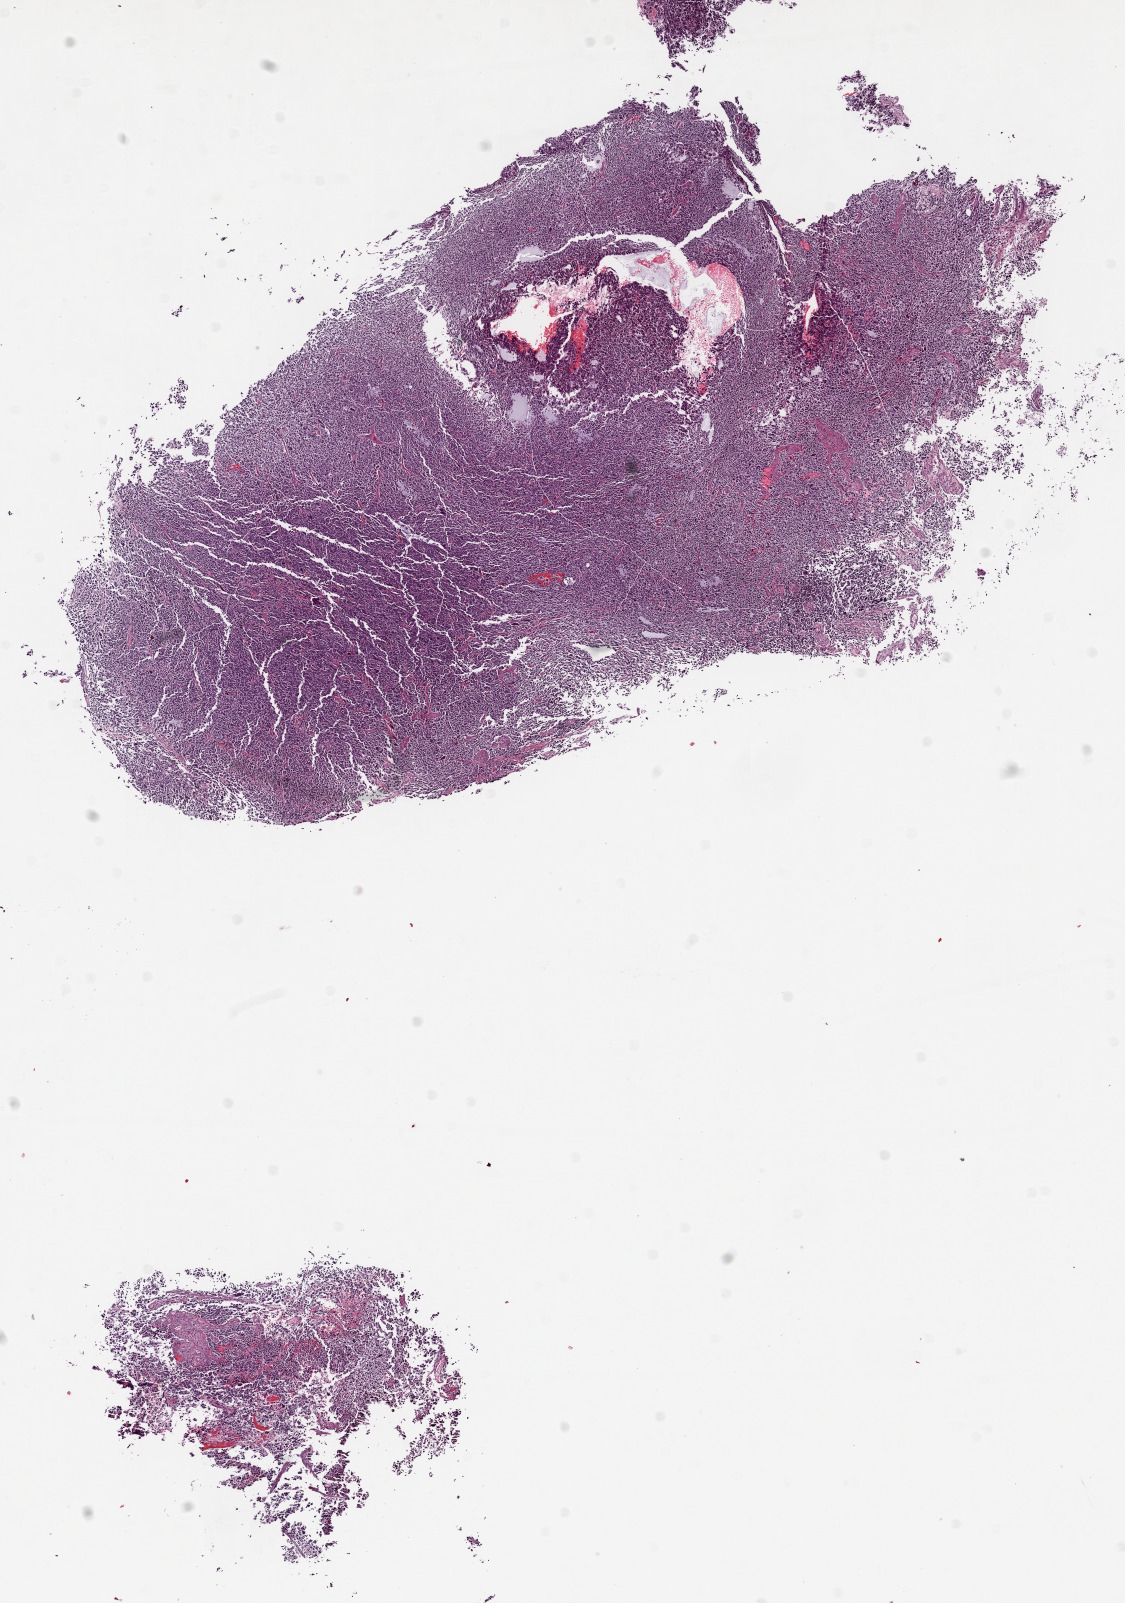
Whole-slide histology image, Hematoxylin and eosin (H&E) stained, whole scanned area (about 9.0 x 12.9 mm, slide scanned at 20x) shown as a low-resolution overview; formalin-fixed paraffin-embedded (FFPE) diagnostic section; brain, primary tumour sample. Male, age 31 years at initial diagnosis.
Diagnosis: Glioblastoma.